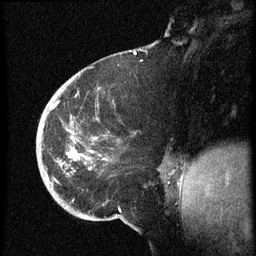
Breast MRI (dynamic contrast-enhanced), one sagittal slice. Position 21 of 60 along the scan axis. Dynamic contrast-enhanced series, image 2 of 3 at this slice position (ordered by acquisition). 1.5 T. TE 4.2 ms, TR 8.4 ms. 256 × 256 image matrix, field of view 200 × 200 mm. Patient: female, 38 years. Case-level facts recorded for this patient, not image findings: setting: breast cancer imaged before/during neoadjuvant chemotherapy; receptor status: HER2-positive.
Annotated regions visible in this slice (semi-automatic segmentation, software-assisted and operator-edited):
- analysis volume of interest (the breast-tissue region the enhancement analysis was run in; not a lesion): box from (x=37, y=74) to (x=173, y=202) px
- tumour enhancement mask (voxels above the 70 % enhancement threshold inside the analysis volume of interest): (x=52, y=103)–(x=106, y=165)